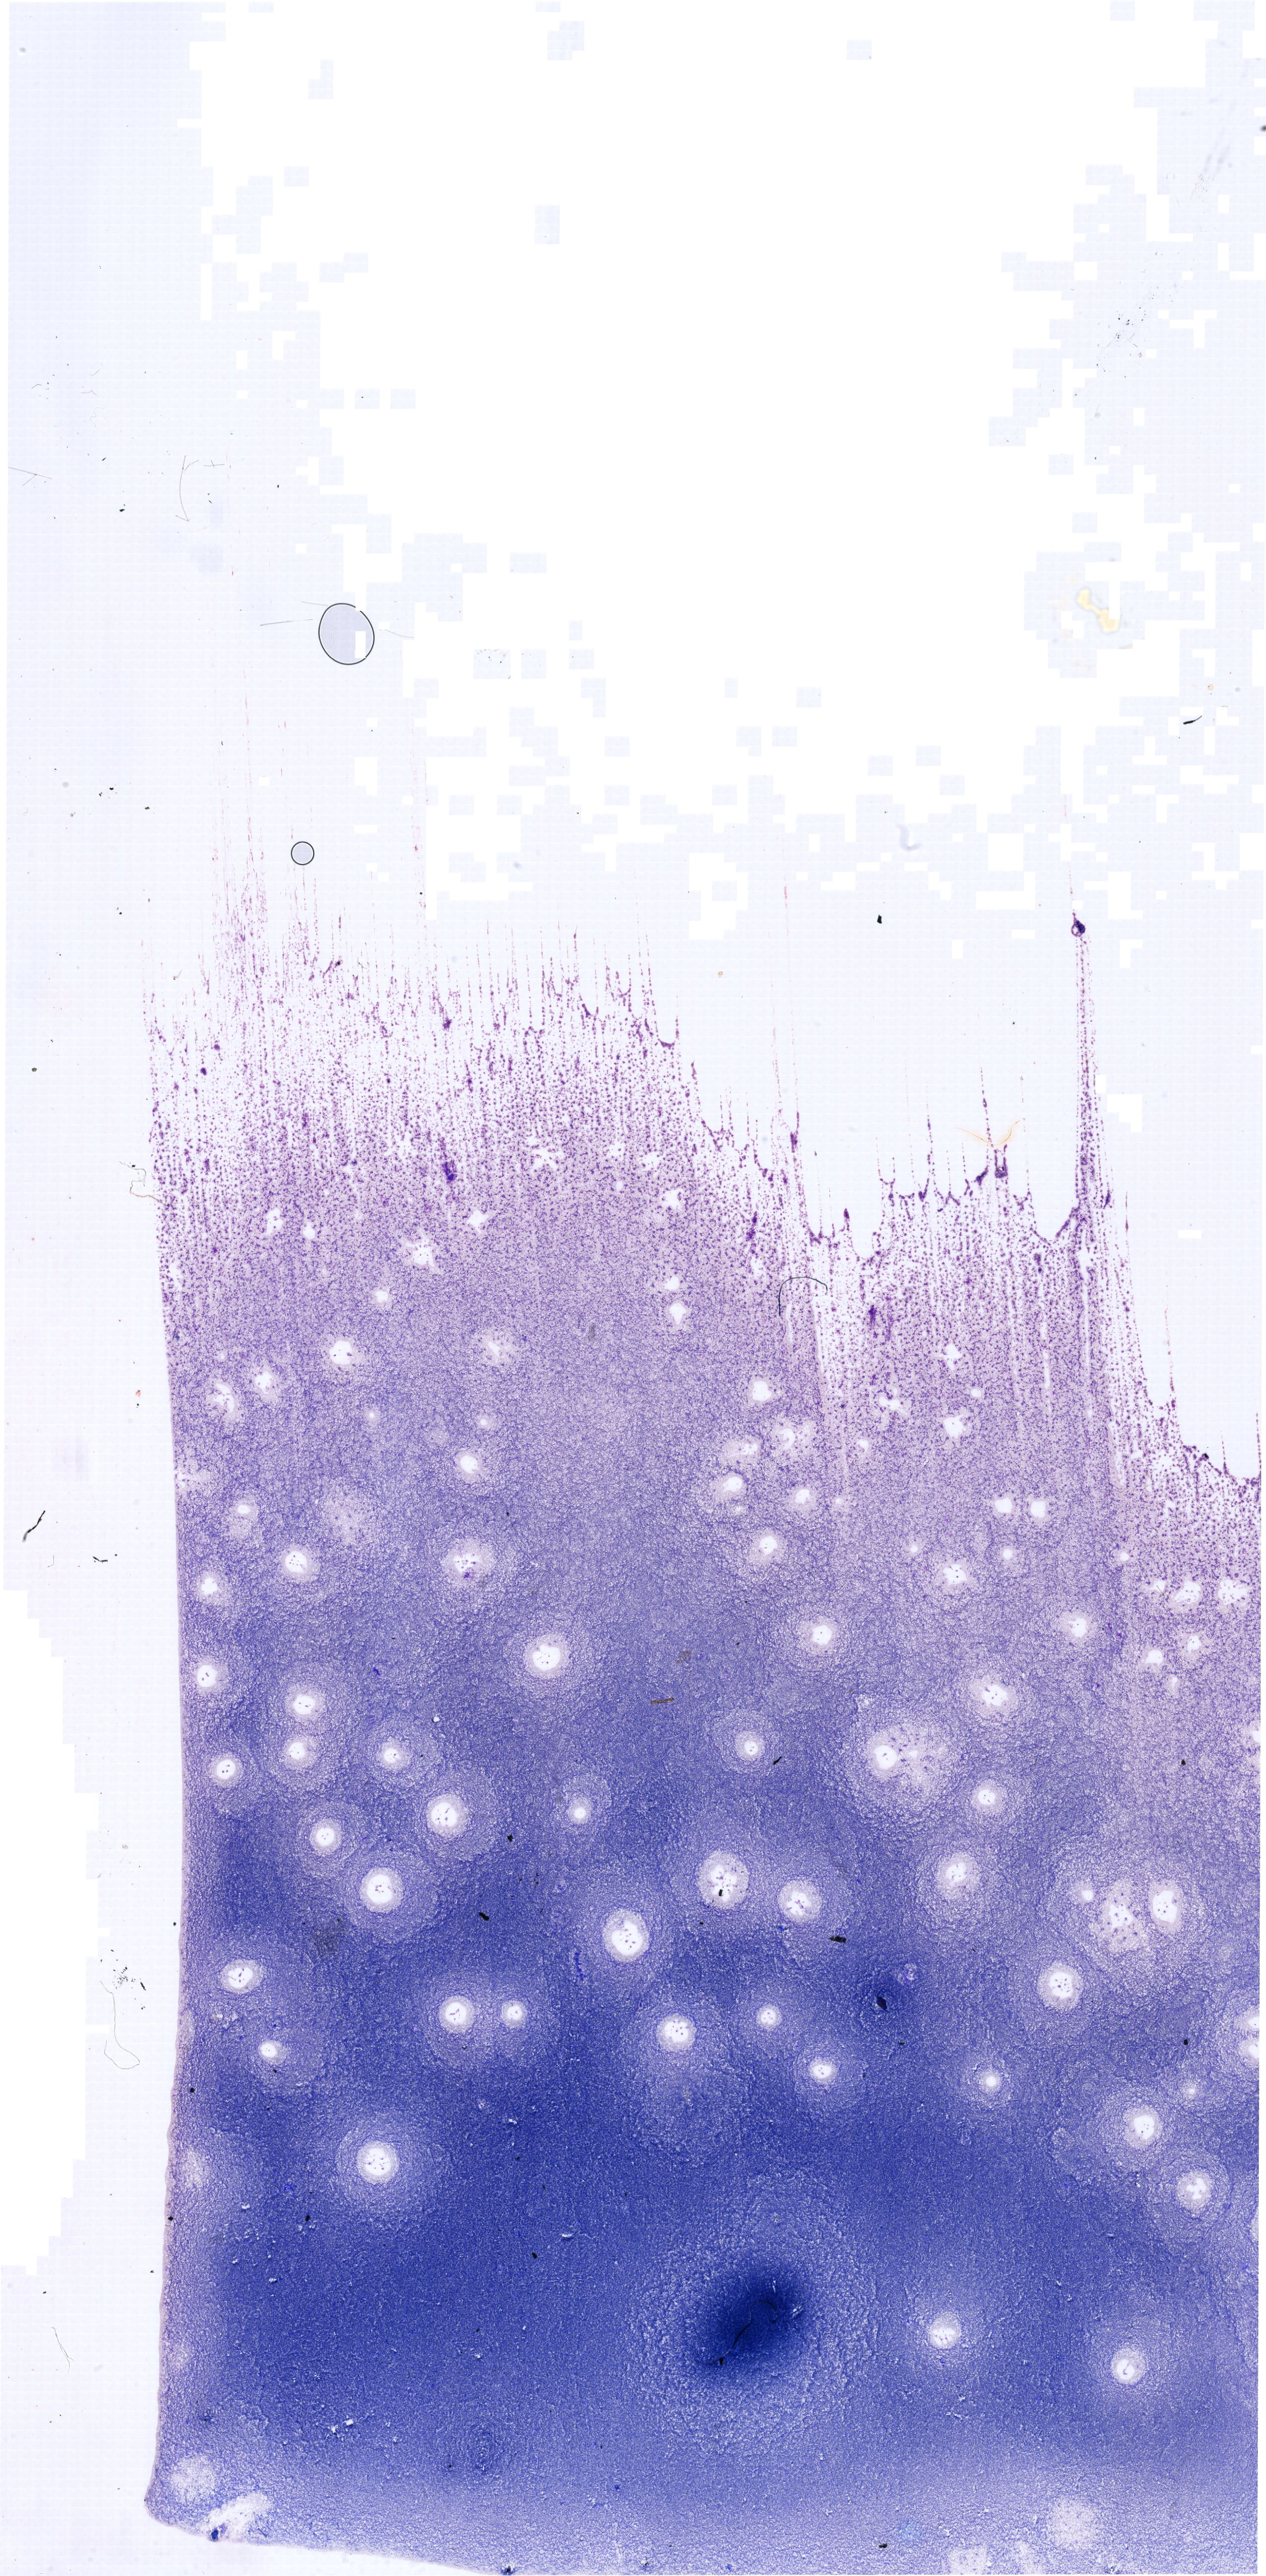
Whole-slide image of a May-Grünwald-Giemsa (MGG)-stained bone marrow aspirate smear — whole scanned area (about 20.5 x 41.7 mm) shown as a low-resolution overview. Male patient.
Diagnosis: T Acute Lymphoblastic Leukemia.